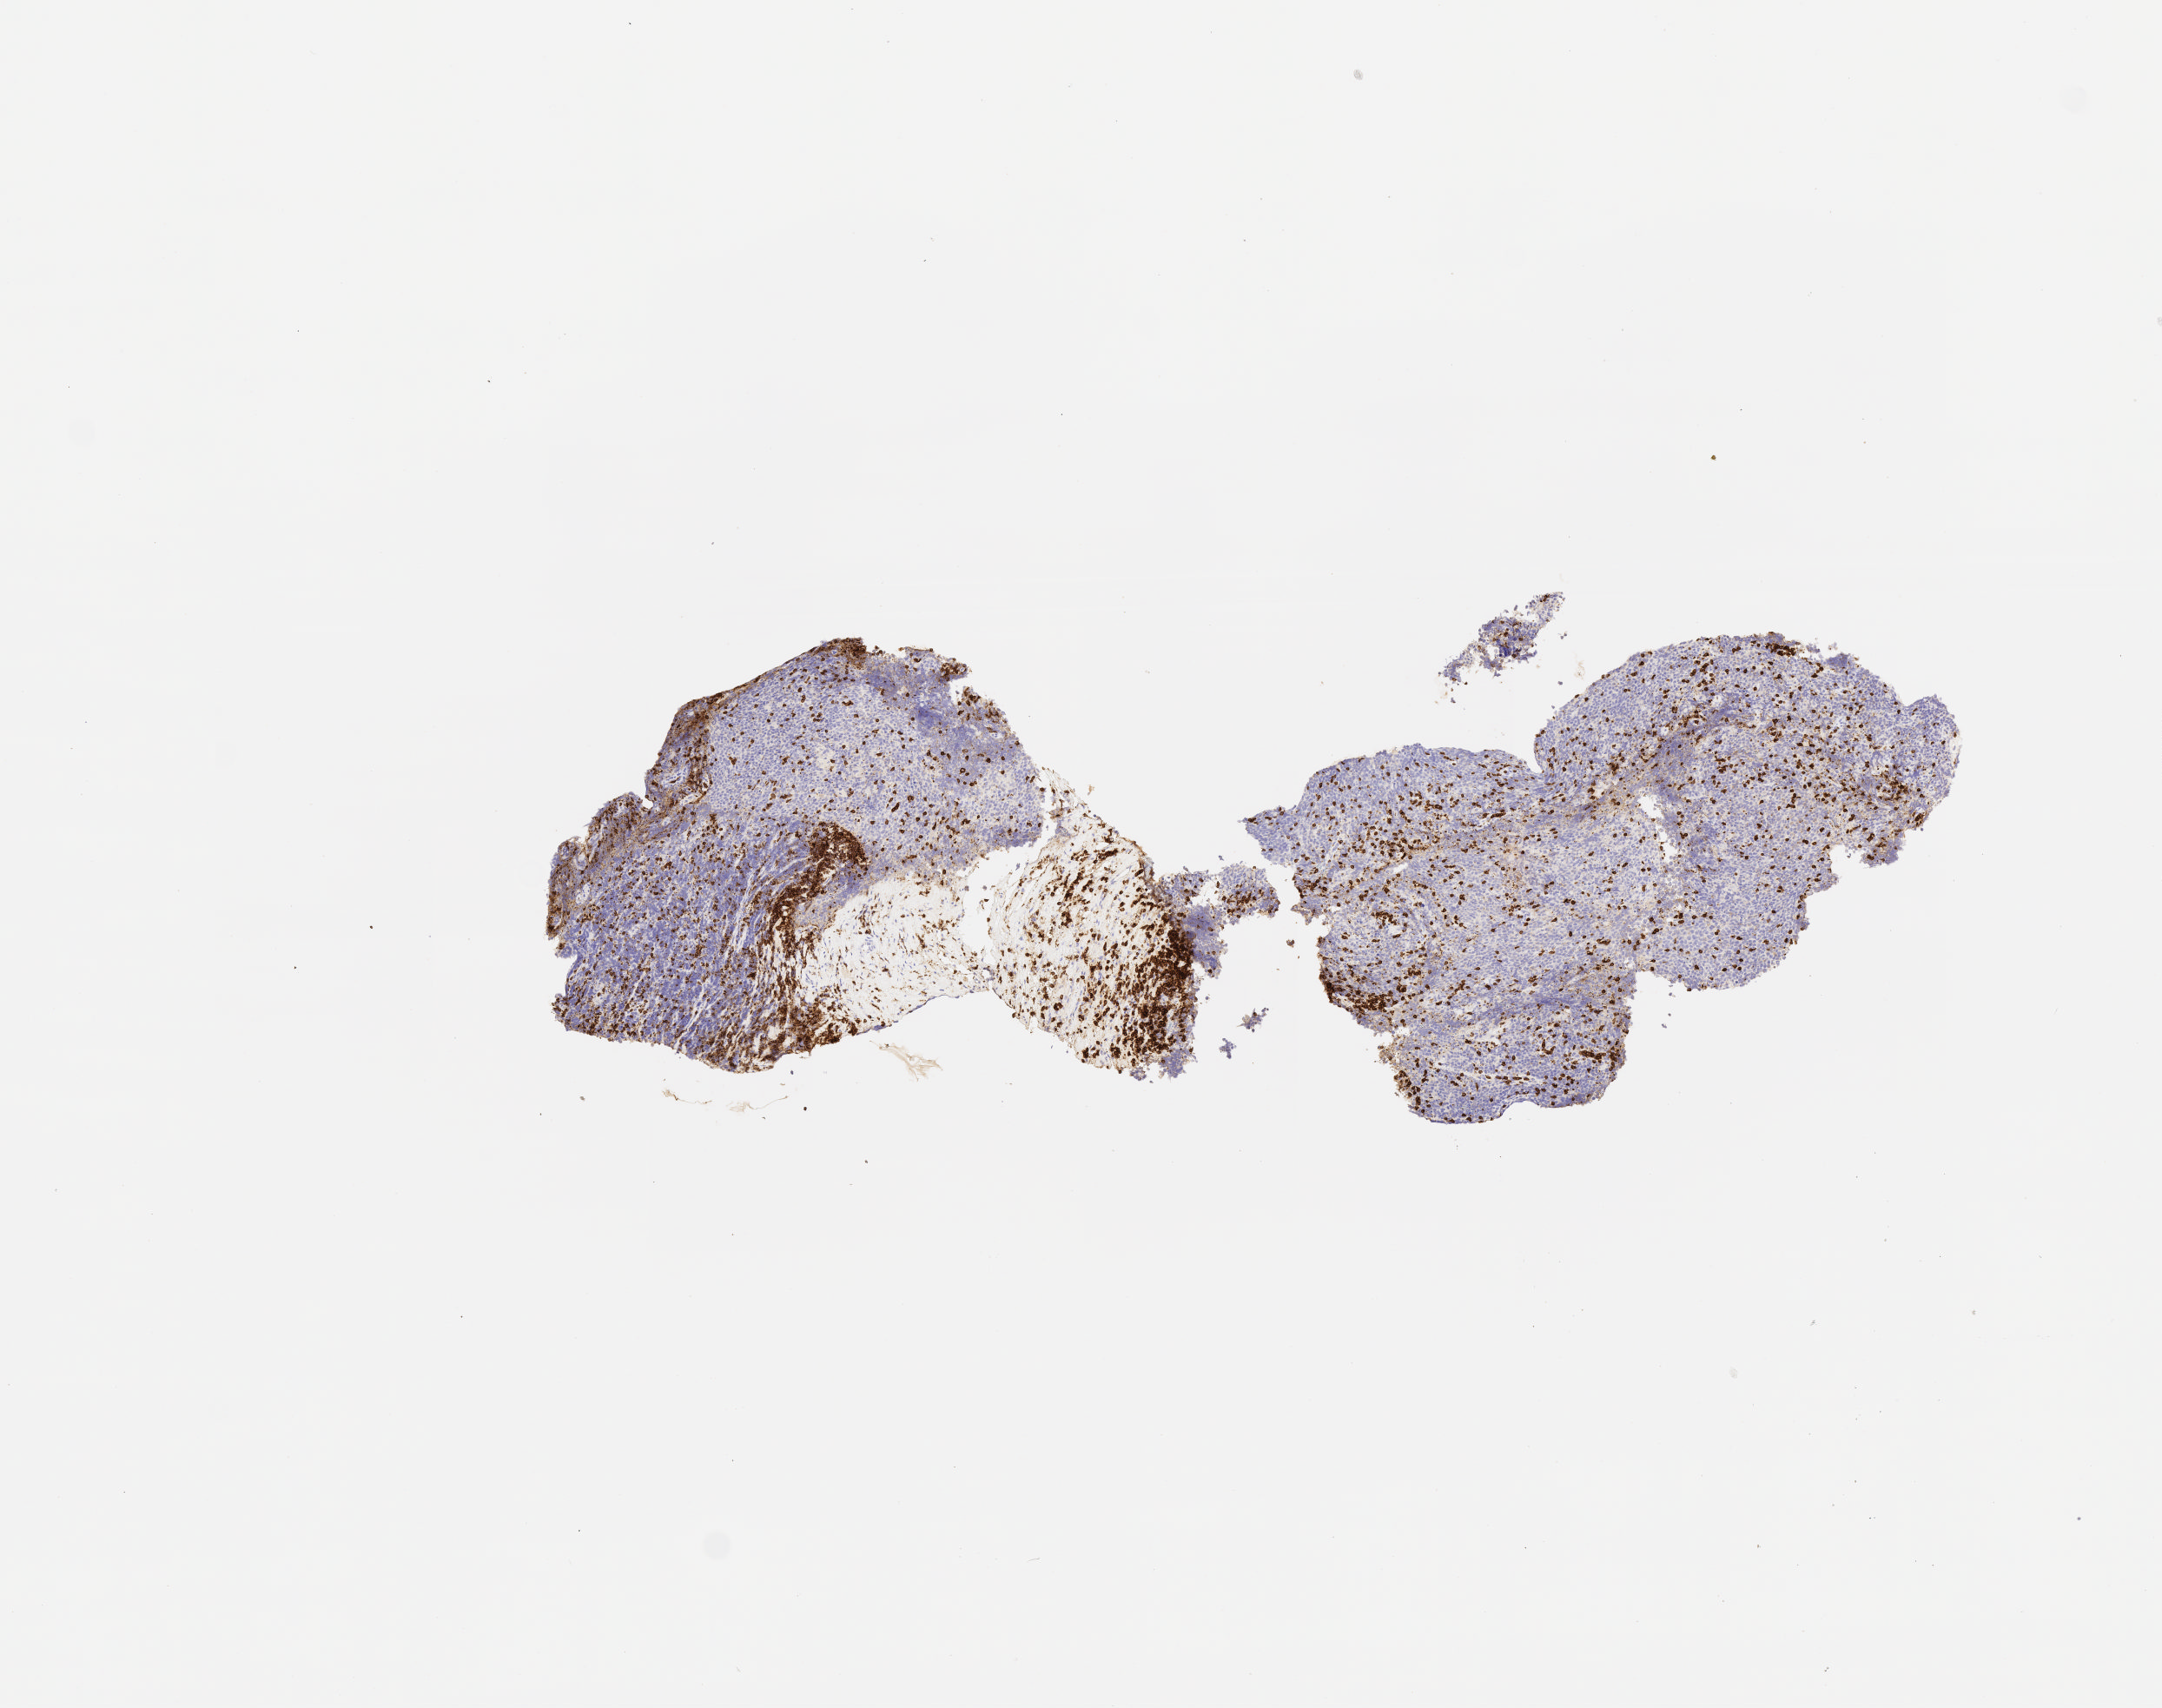
Whole-slide image, immunohistochemical stain for CD3, low-resolution overview of the scanned area, about 5.0 x 4.0 mm, specimen: tumor tissue. Patient male; aged 15.
Histologic diagnosis: Burkitt lymphoma, NOS.